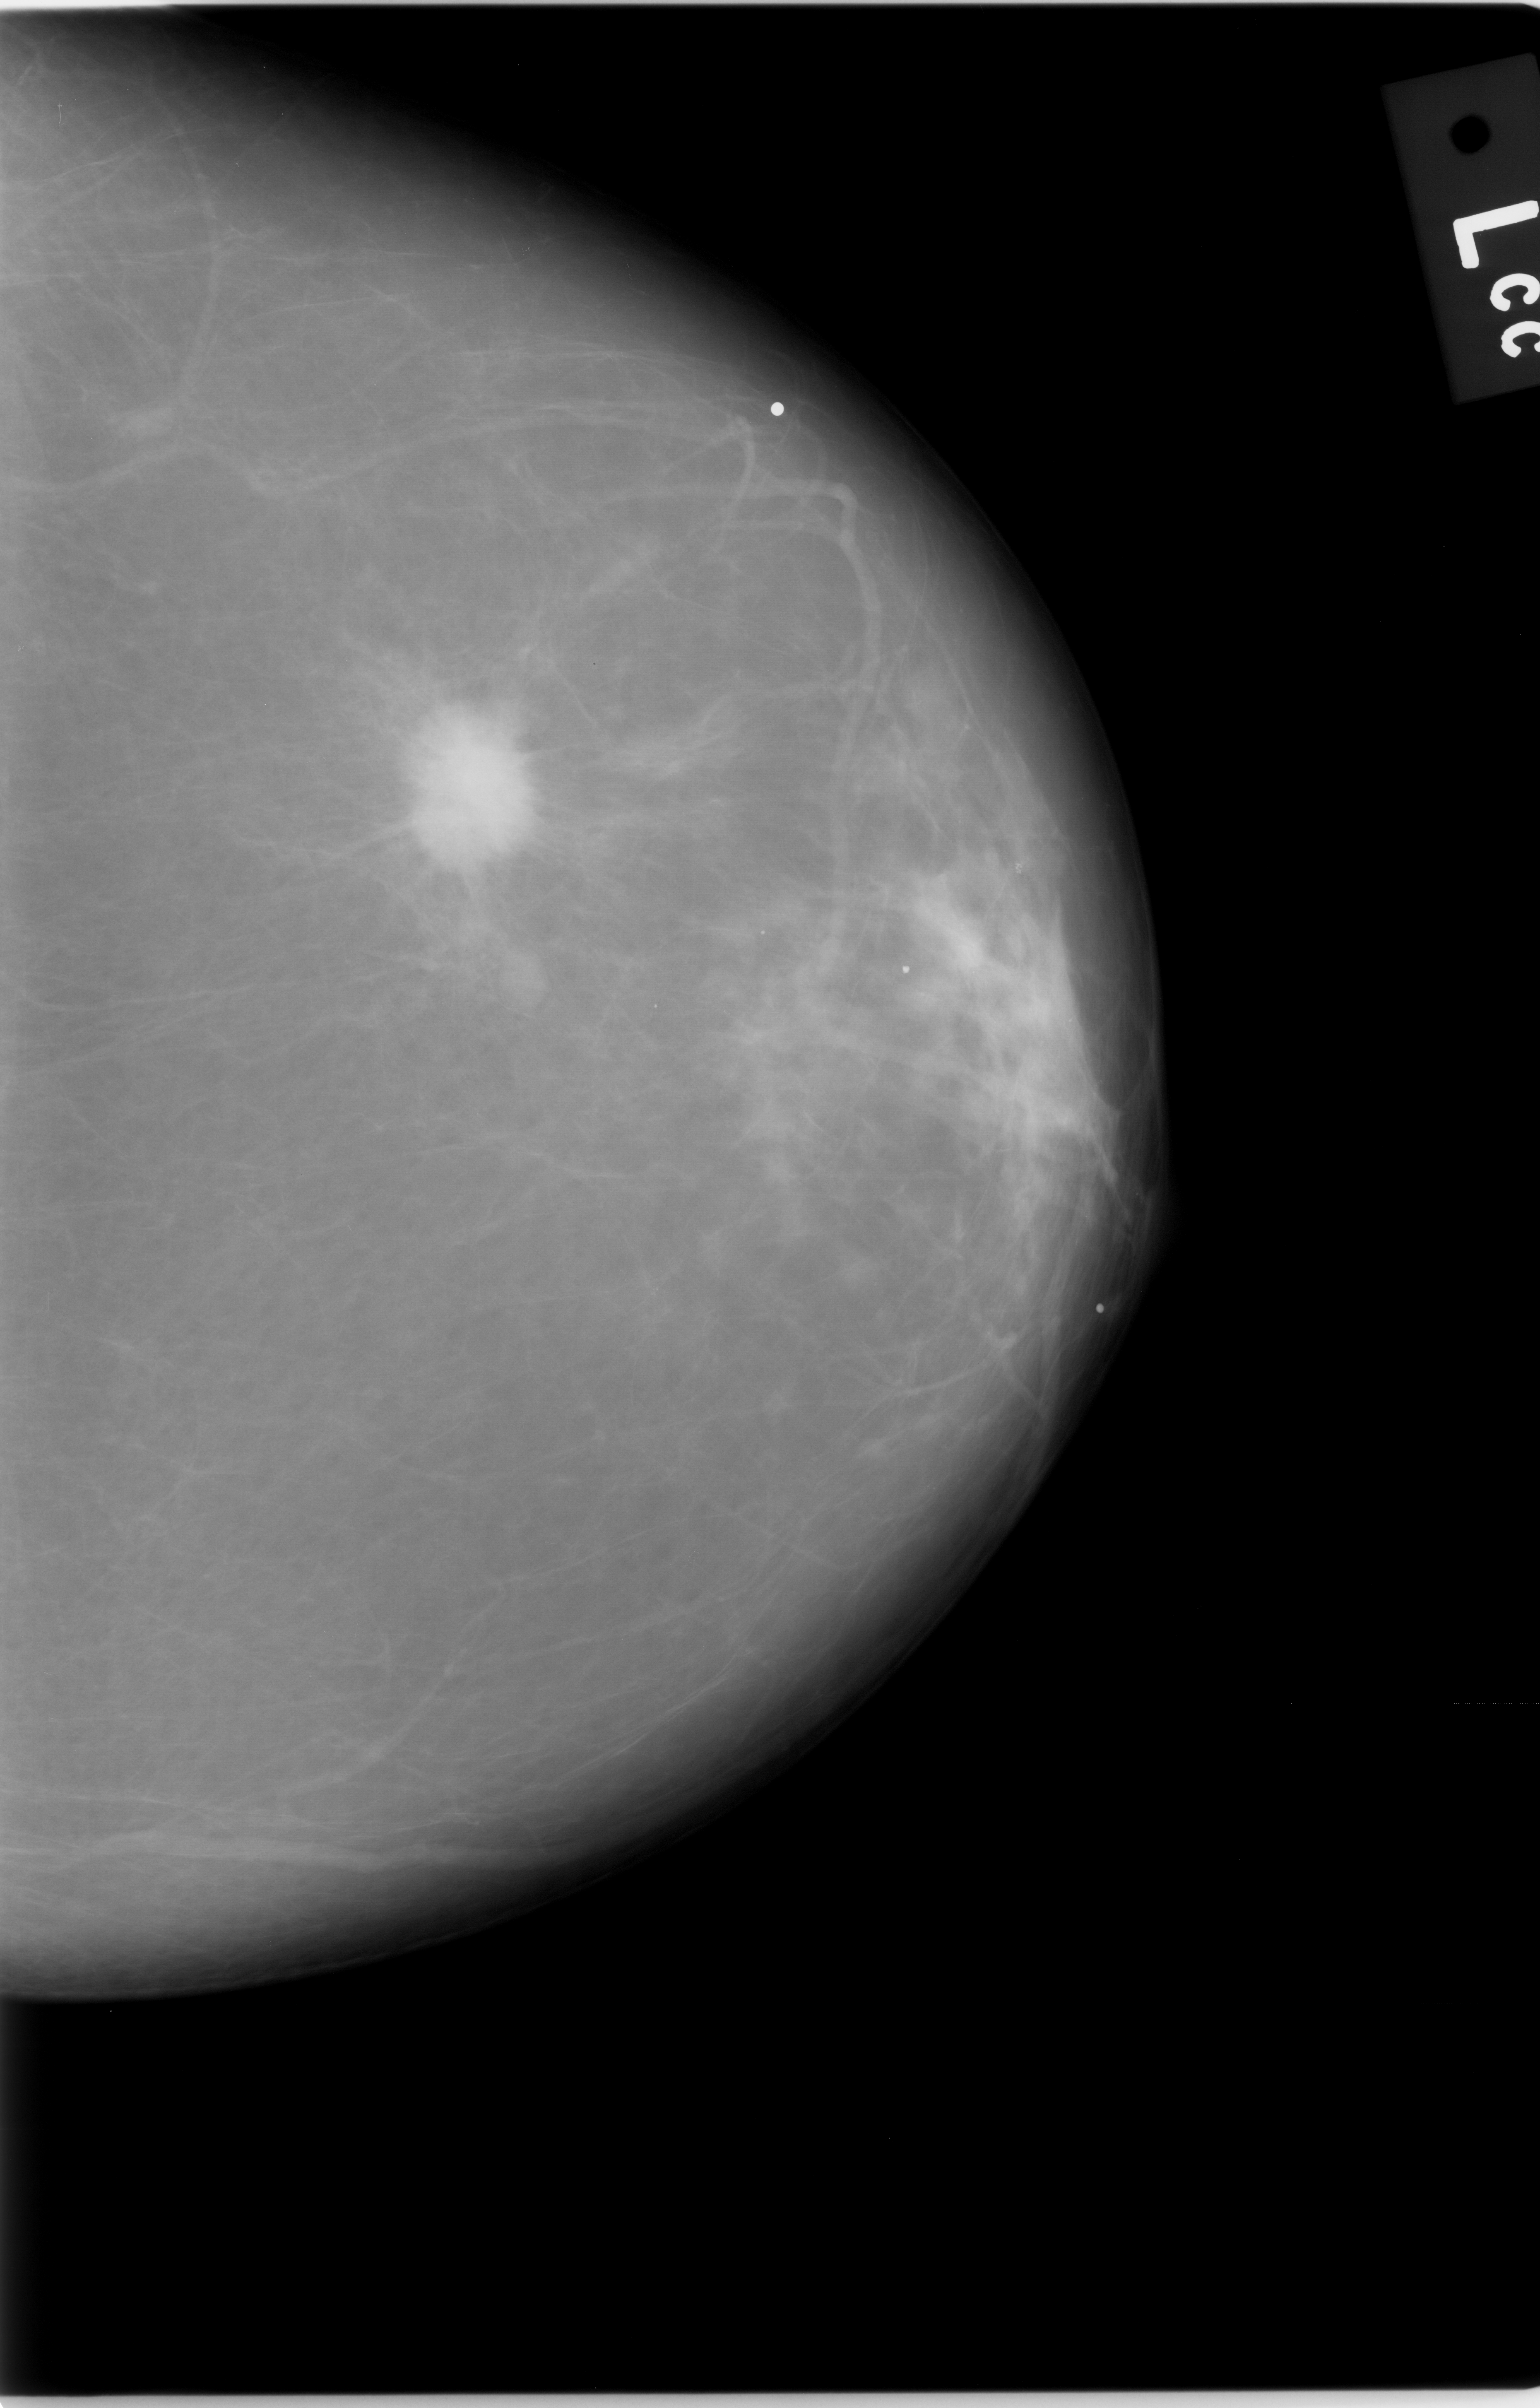
Scanned film-screen mammogram; left breast; craniocaudal (CC) view; BI-RADS breast density category 1 (scale 1–4); 1540 × 2408 image matrix.
Marked abnormalities (boxes around the expert regions of interest):
- mass, shape irregular, margins ill defined; BI-RADS assessment category 5; pathology result (as recorded, not read from the image): malignant: bounding box (x1, y1, x2, y2) in pixels: (376, 694, 554, 903)